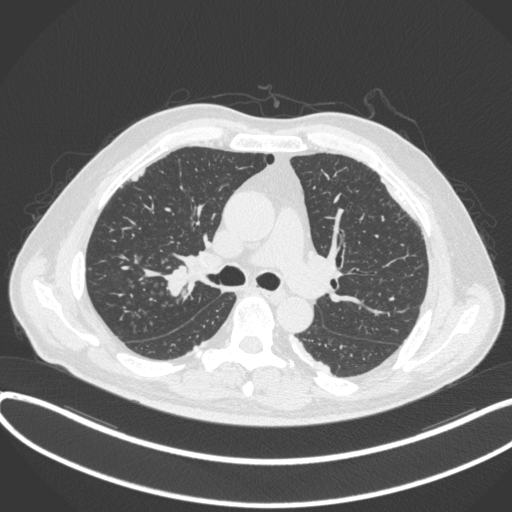
Chest CT, one axial slice; slice 265 of 455 in the series (ordered by position); reconstruction kernel B31f; lung window (W 1500 / L -600 HU); 1 mm slice thickness; 512 × 512 image matrix, field of view 400 × 400 mm. Patient: male, 58 years. Case-level facts recorded for this patient, not image findings: clinical TNM (as recorded): T1c N0 M0.
Outlined on this slice (bounding box drawn by a radiologist):
- lung tumour (recorded histology: squamous cell carcinoma): bounding box <162,261,193,299> (left, top, right, bottom; pixels)